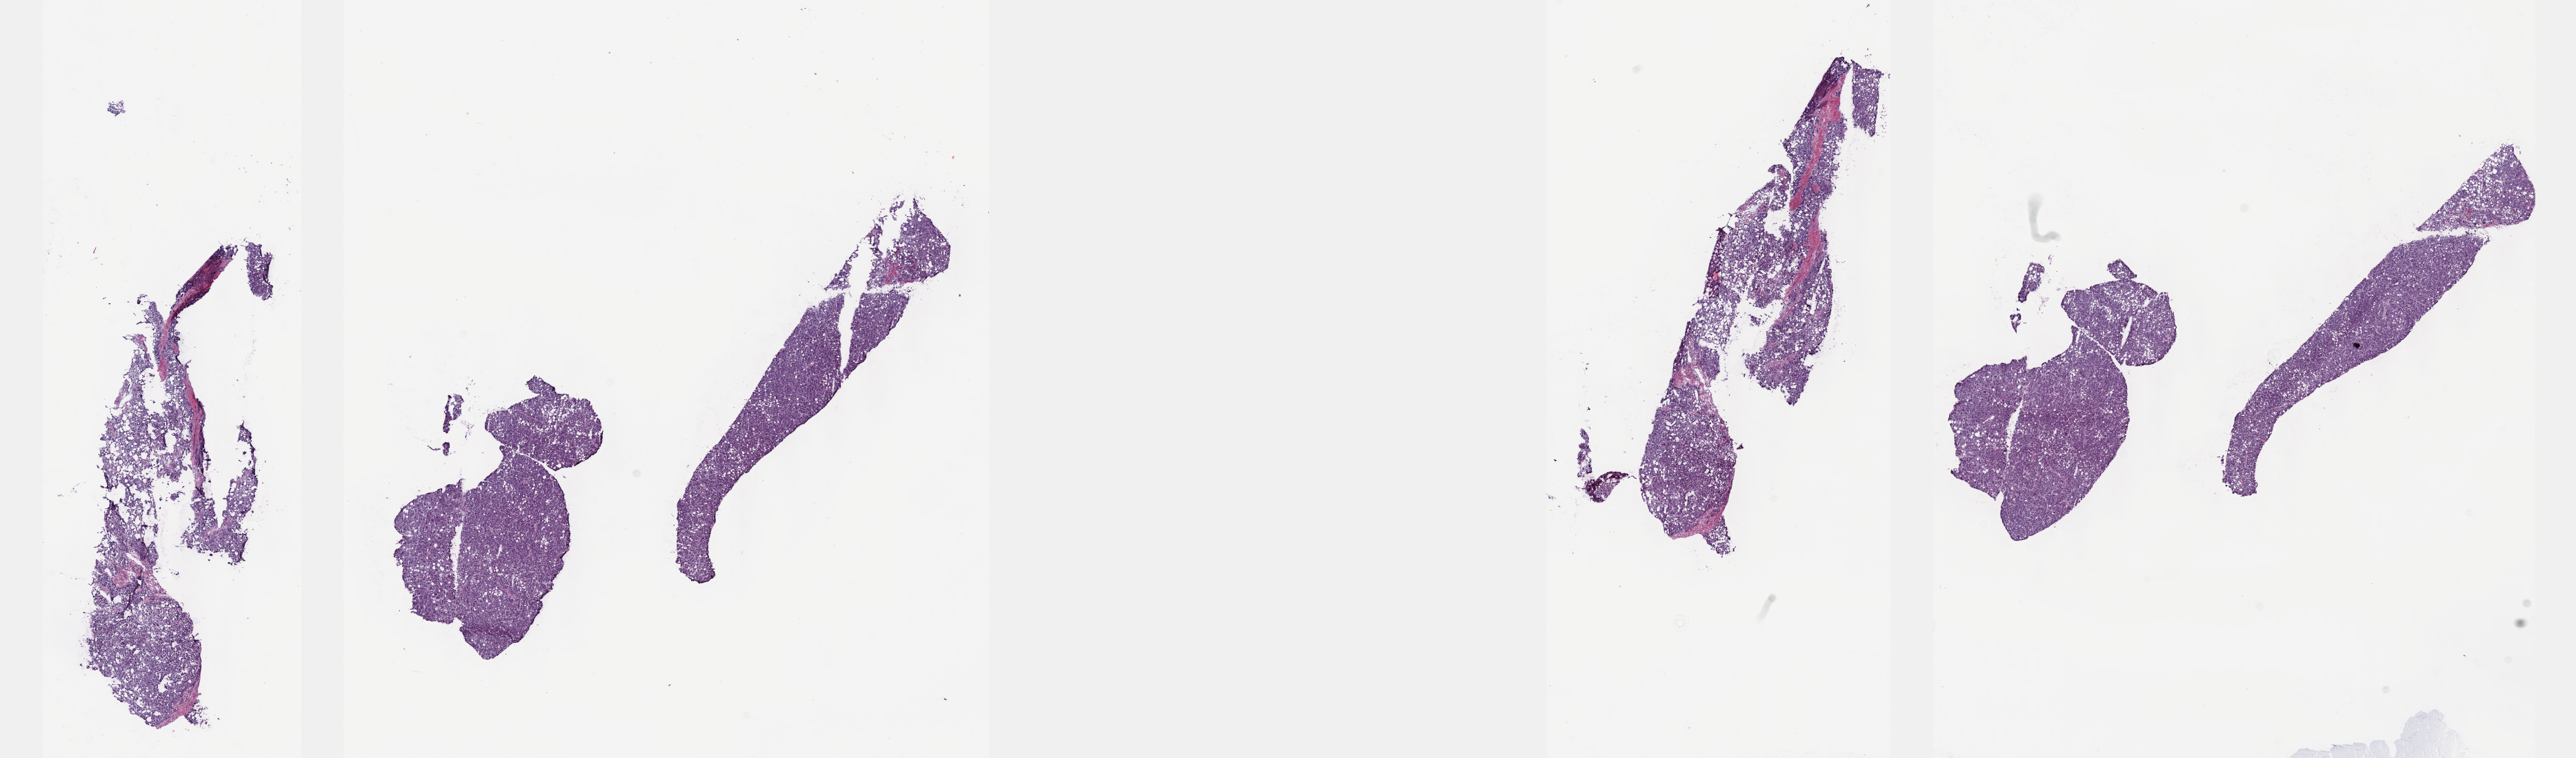
Whole-slide histology image, Hematoxylin and eosin (H&E) stained — a low-resolution overview of the entire scanned area, about 30.2 x 8.9 mm (slide scanned at 40x); frozen section; liver, primary tumour sample. Female patient; age at initial diagnosis 68 years. Slide review estimates, as recorded: tumour cells 80%, tumour nuclei 80%.
Pathologic diagnosis: Hepatocellular carcinoma, NOS.